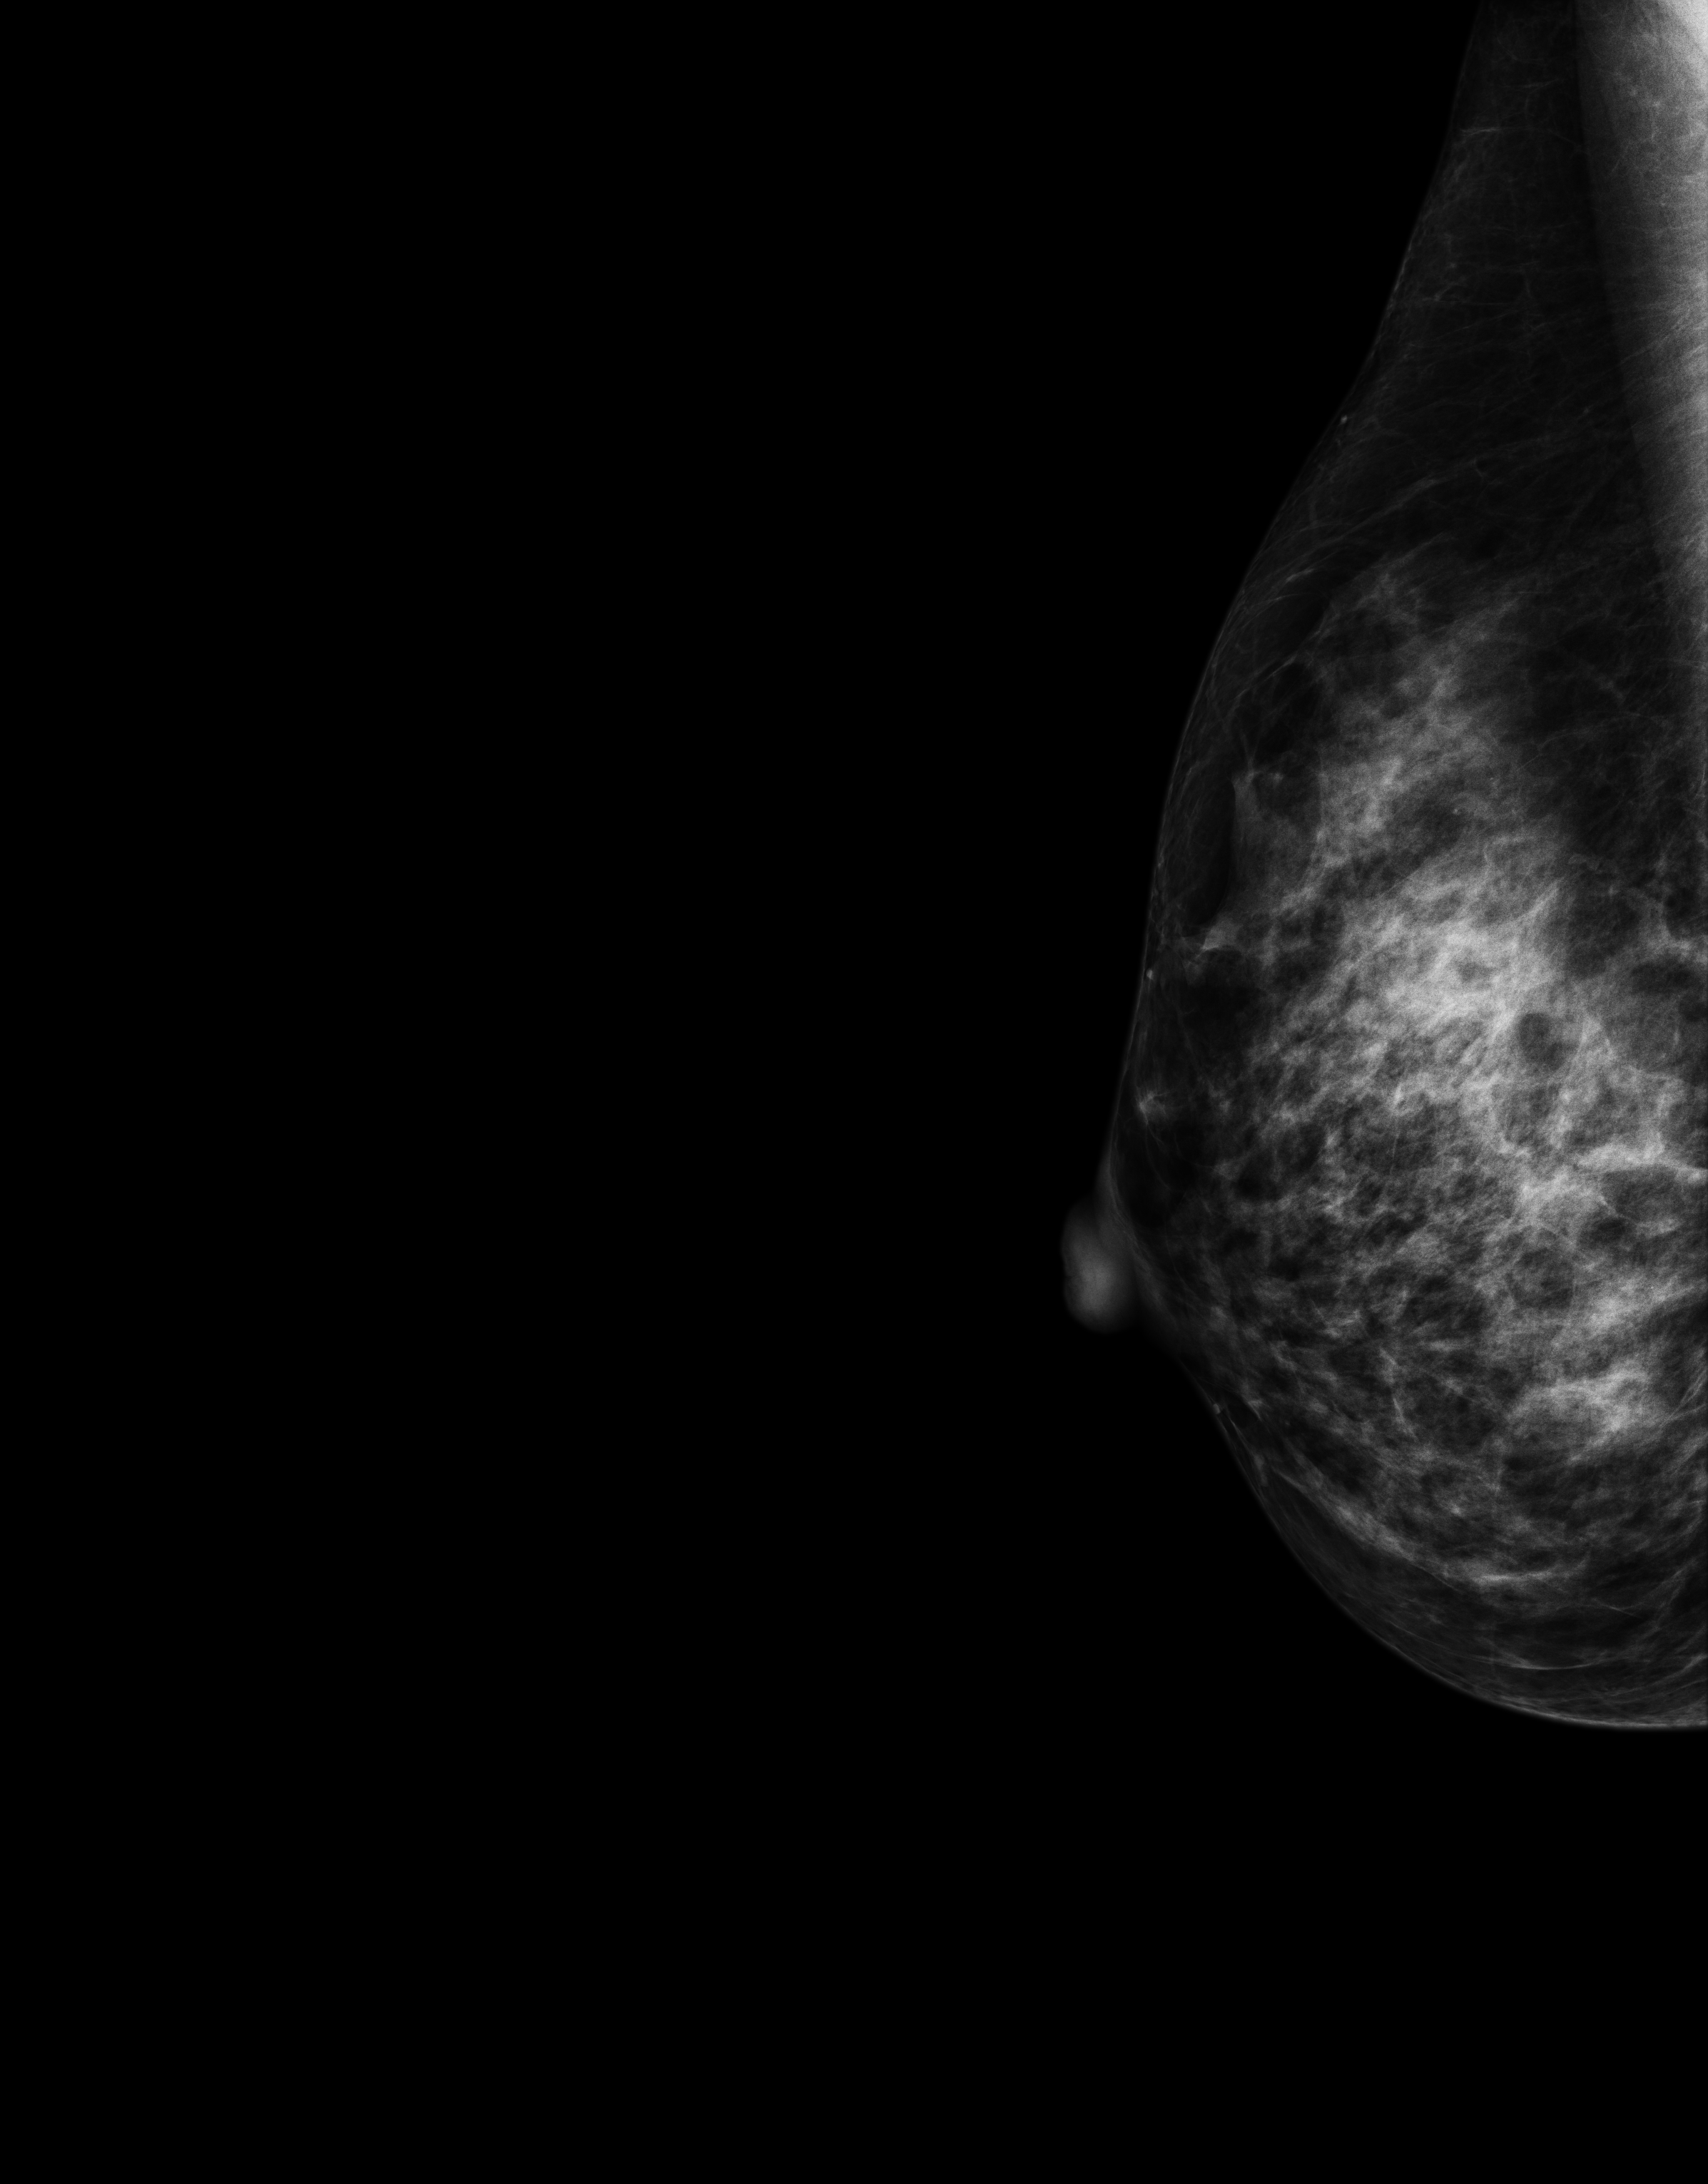
Full-field digital mammogram (FFDM); right breast; laterally exaggerated craniocaudal (XCCL) view; screening examination; compressed breast thickness 65 mm; system: Senographe Essential ADS_56.21.3. Patient aged 42 years (female).
- BI-RADS breast density category at the screening exam (both breasts, scale 1–4): 4
- final BI-RADS category for the screening round (tomosynthesis exam, both breasts): category 1
- recall: no recall after this screen